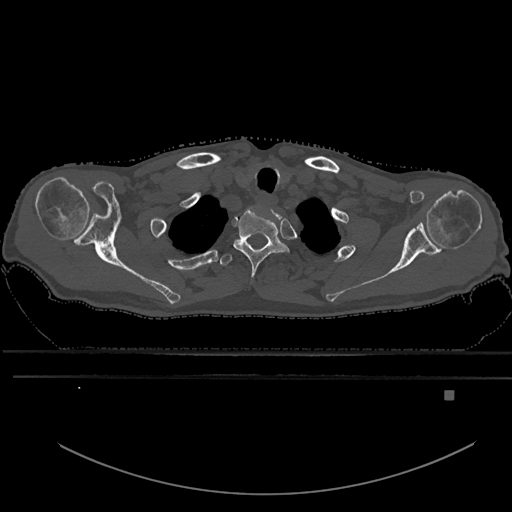
CT including the spine, one axial slice; slice 533 of 969 in the series (ordered by position); bone window (W 1800 / L 400 HU); 0.5 mm slice thickness; 512 × 512 image matrix, field of view 456 × 456 mm. Patient: male, 82 years. From the clinical record (not read from this slice): primary cancer: prostate; vertebrae with lytic lesions (as recorded): T11, T9, T8, T2.
Outlined on this slice (semi-automatic segmentation, software-assisted and operator-edited):
- T1 vertebra: bounding box <233,210,288,278> (left, top, right, bottom; pixels)
- T2 vertebra: <219,238,246,266>